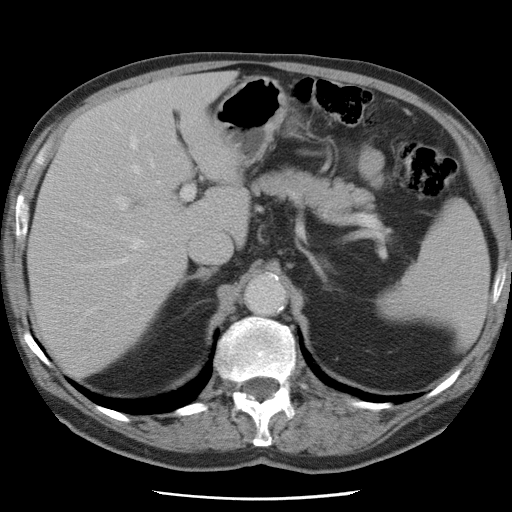
Contrast-enhanced abdominal CT, one axial slice. Intravenous contrast given. Soft-tissue window (W 400 / L 40 HU). 5 mm slice thickness. 512 × 512 image matrix, field of view 337 × 337 mm. Male patient, age 75 years. From the clinical record (not read from this slice): diagnosis: colorectal cancer liver metastases, imaged before liver resection; multiple liver metastases: yes; largest metastasis: 2.4 cm.
Structures marked on this image (outlined manually by an expert reader):
- hepatic veins: bounding box (x1, y1, x2, y2) in pixels: (54, 137, 160, 271)
- liver: (29, 75, 250, 378)
- planned liver remnant (the part of the liver to remain after resection): (29, 124, 194, 378)
- portal vein (with intrahepatic branches): (115, 186, 196, 215)